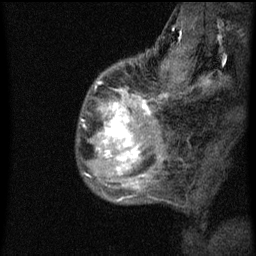
Breast MRI (dynamic contrast-enhanced), one sagittal slice; position 14 of 60 along the scan axis; dynamic contrast-enhanced series, image 2 of 3 at this slice position (ordered by acquisition); 1.5 T; TE 4.2 ms, TR 8 ms; 2 mm slice thickness; 256 × 256 image matrix, field of view 180 × 180 mm. Patient: female, 50 years.
Structures marked on this image (semi-automatically segmented with operator editing):
- analysis volume of interest (the breast-tissue region the enhancement analysis was run in; not a lesion): bounding box [x1, y1, x2, y2] px = [78, 66, 141, 187]
- tumour enhancement mask (voxels above the 70 % enhancement threshold inside the analysis volume of interest): [99, 102, 140, 171]